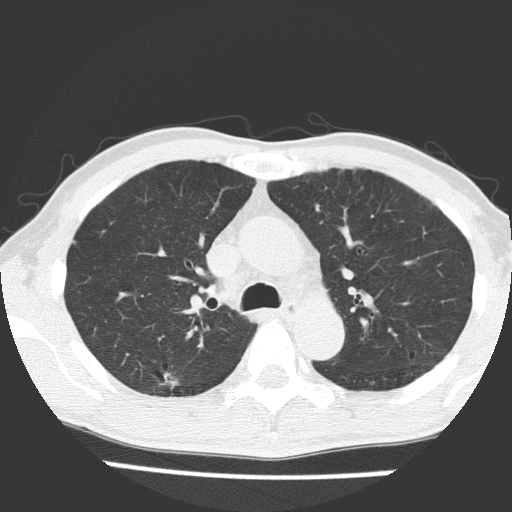
Low-dose screening chest CT, one axial slice. Position 111 of 160 along the scan axis. 120 kVp. Lung window (W 1500 / L -600 HU). 2 mm slice thickness. 512 × 512 image matrix, field of view 309 × 309 mm.
Structures marked on this image (outlined manually by an expert reader):
- lesion 1 (tumor, upper lobe of right lung): bounding box <159,372,179,389> (left, top, right, bottom; pixels)